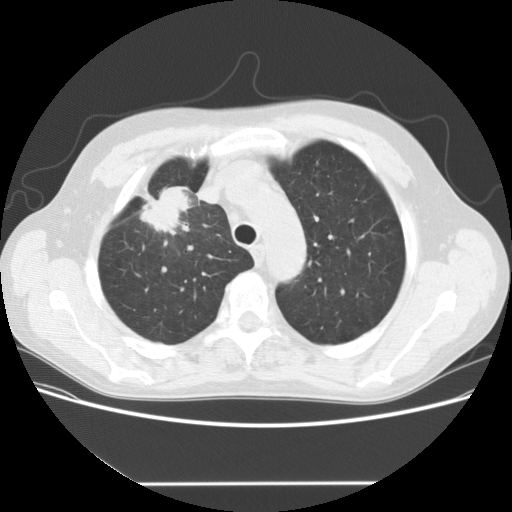
Chest CT (low-dose screening protocol), one axial image; first (baseline) screen; lung window (W 1500 / L -600 HU); slice 33 of 153 in the series. Male, age 56 years at enrolment. Current smoker at enrolment.
Expert reader's lesion annotation, box from (x=128, y=174) to (x=210, y=242) px. The screening reader recorded 2 non-calcified nodules or masses ≥4 mm on this exam (right upper lobe, right middle lobe); which of them this box marks is not recorded. Later outcome: lung cancer diagnosed 120 days after this screen — adenocarcinoma, NOS, right upper lobe, stage IIIA (AJCC 6th edition), 34 mm at pathology.